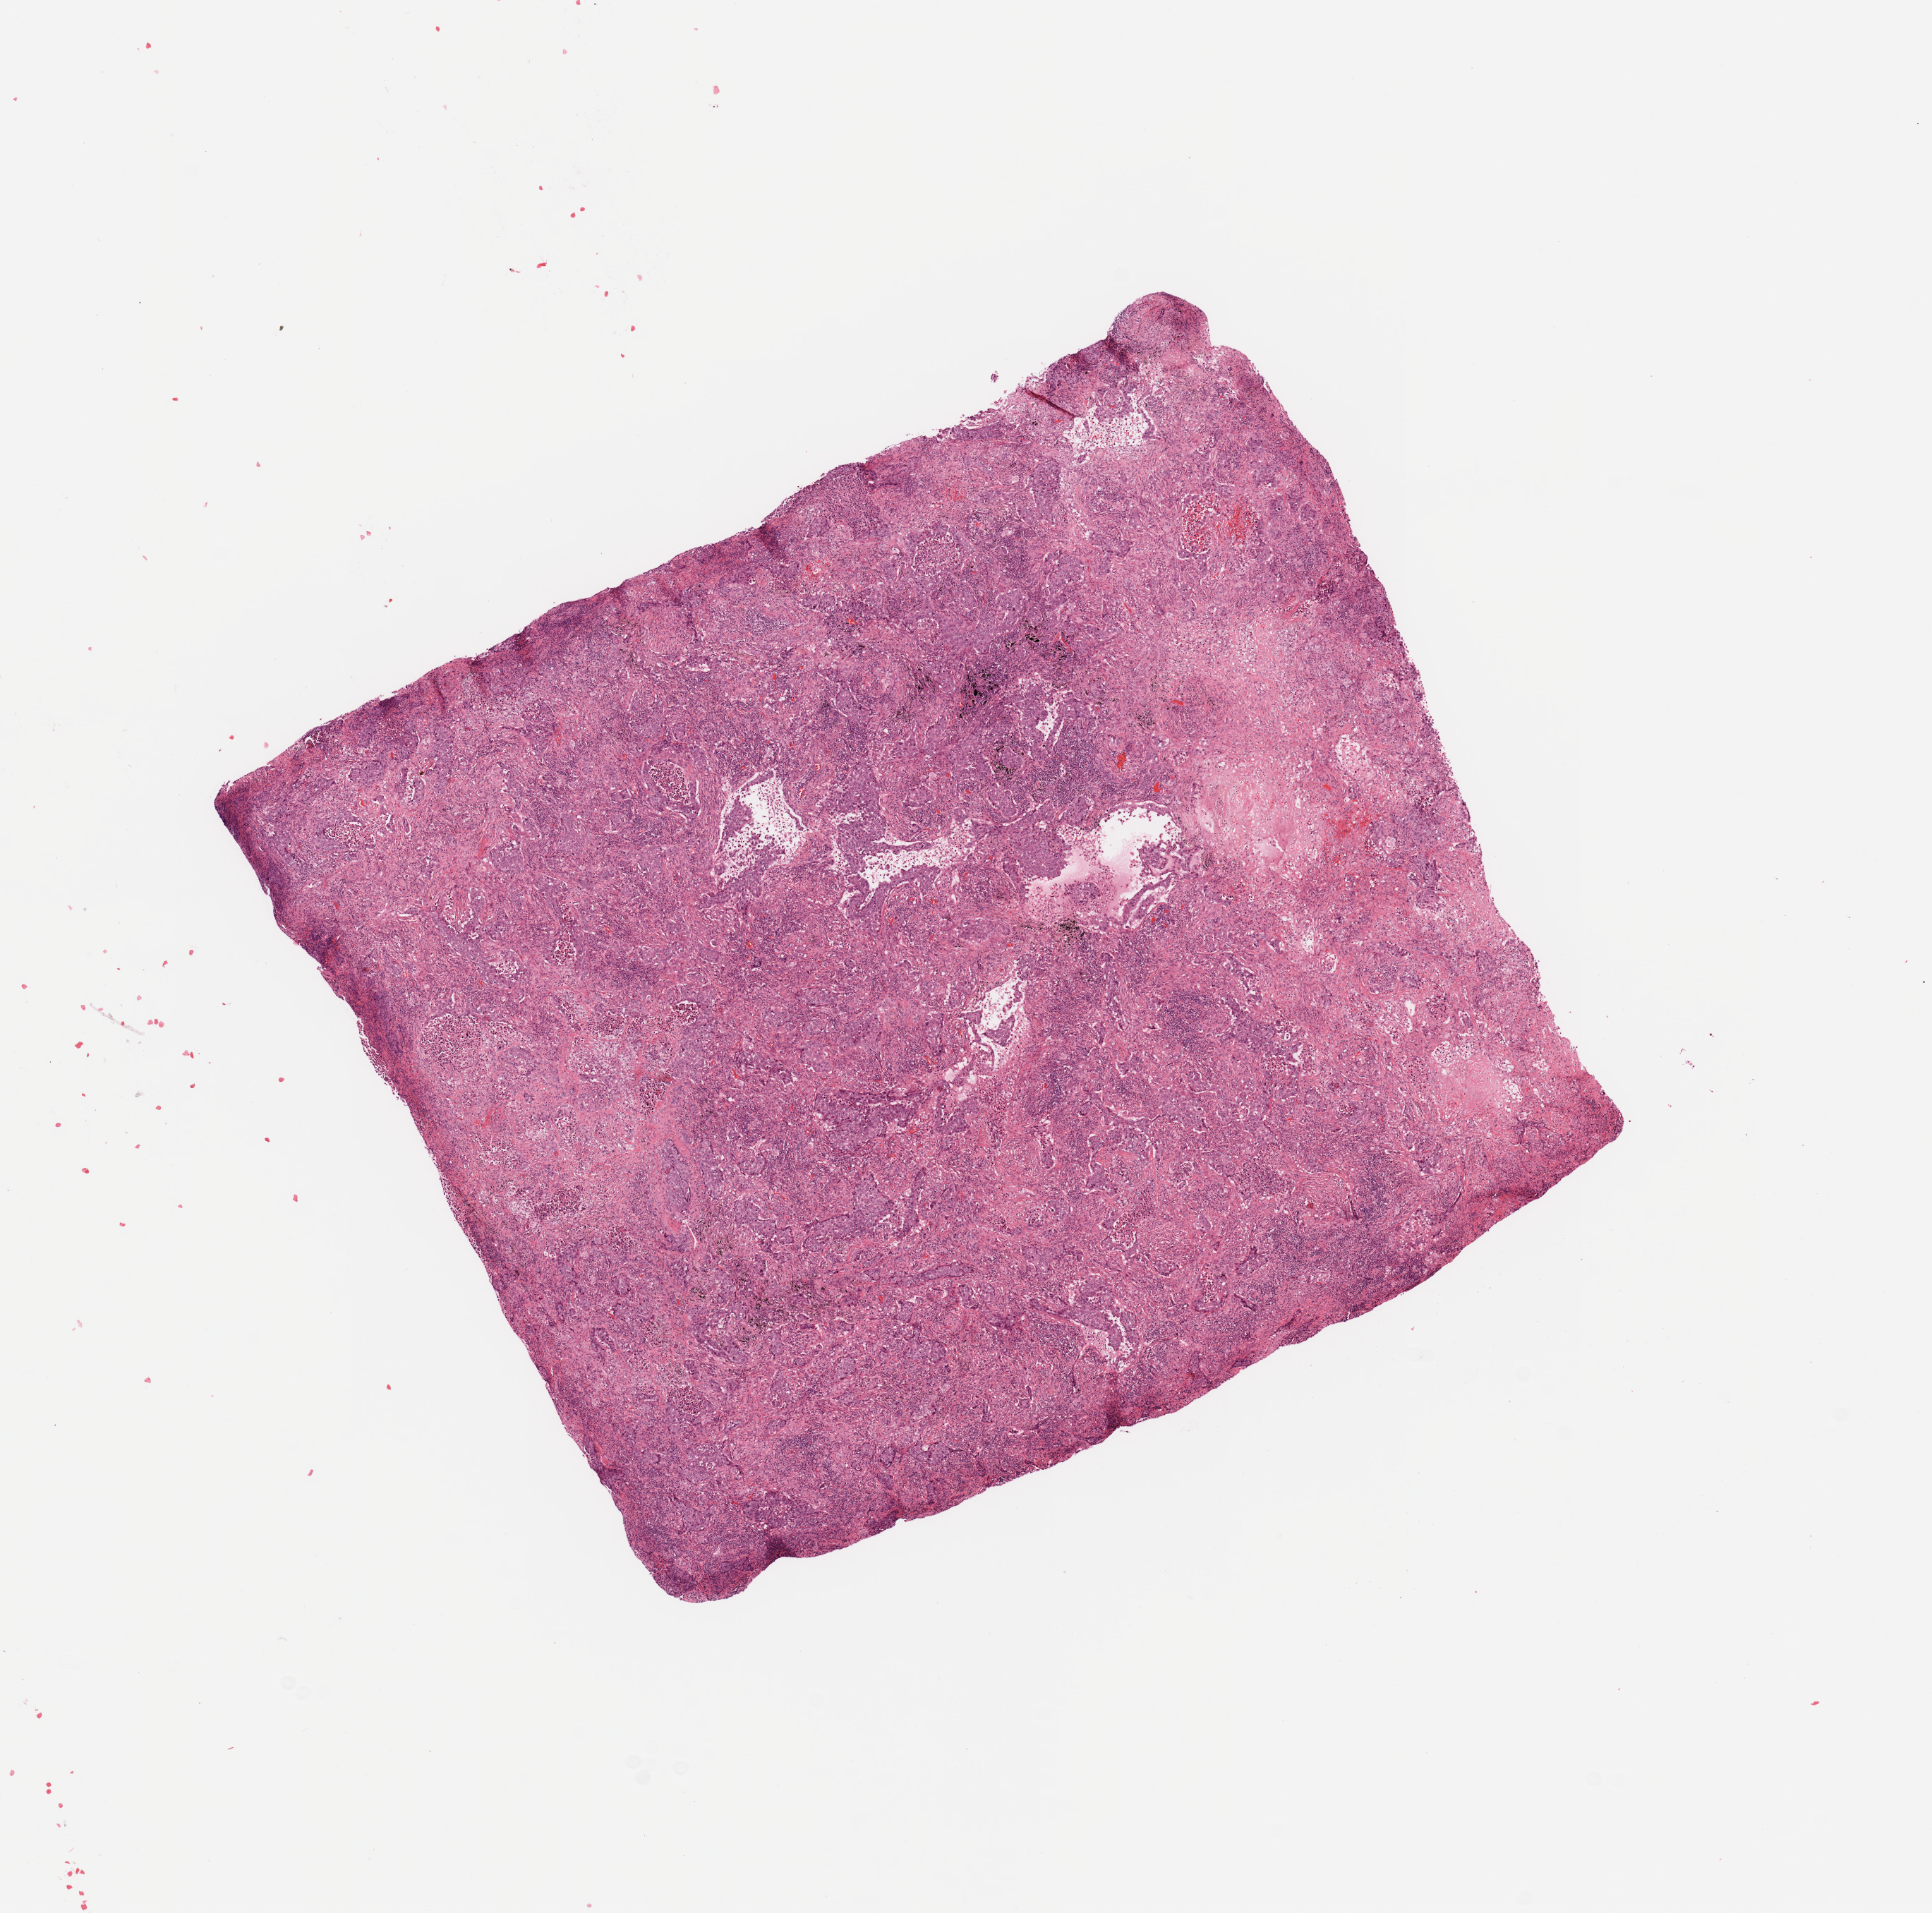
Whole-slide histology image, H&E-stained, low-resolution overview of the scanned area, about 10.8 x 10.7 mm; lung, tumour tissue. Male, 72 y/o. Histologic grade: G3 (poorly differentiated).
AJCC pathologic stage: IIB. Primary tumour site (as recorded): left lower lobe. Histologic diagnosis: Adenocarcinoma, NOS.